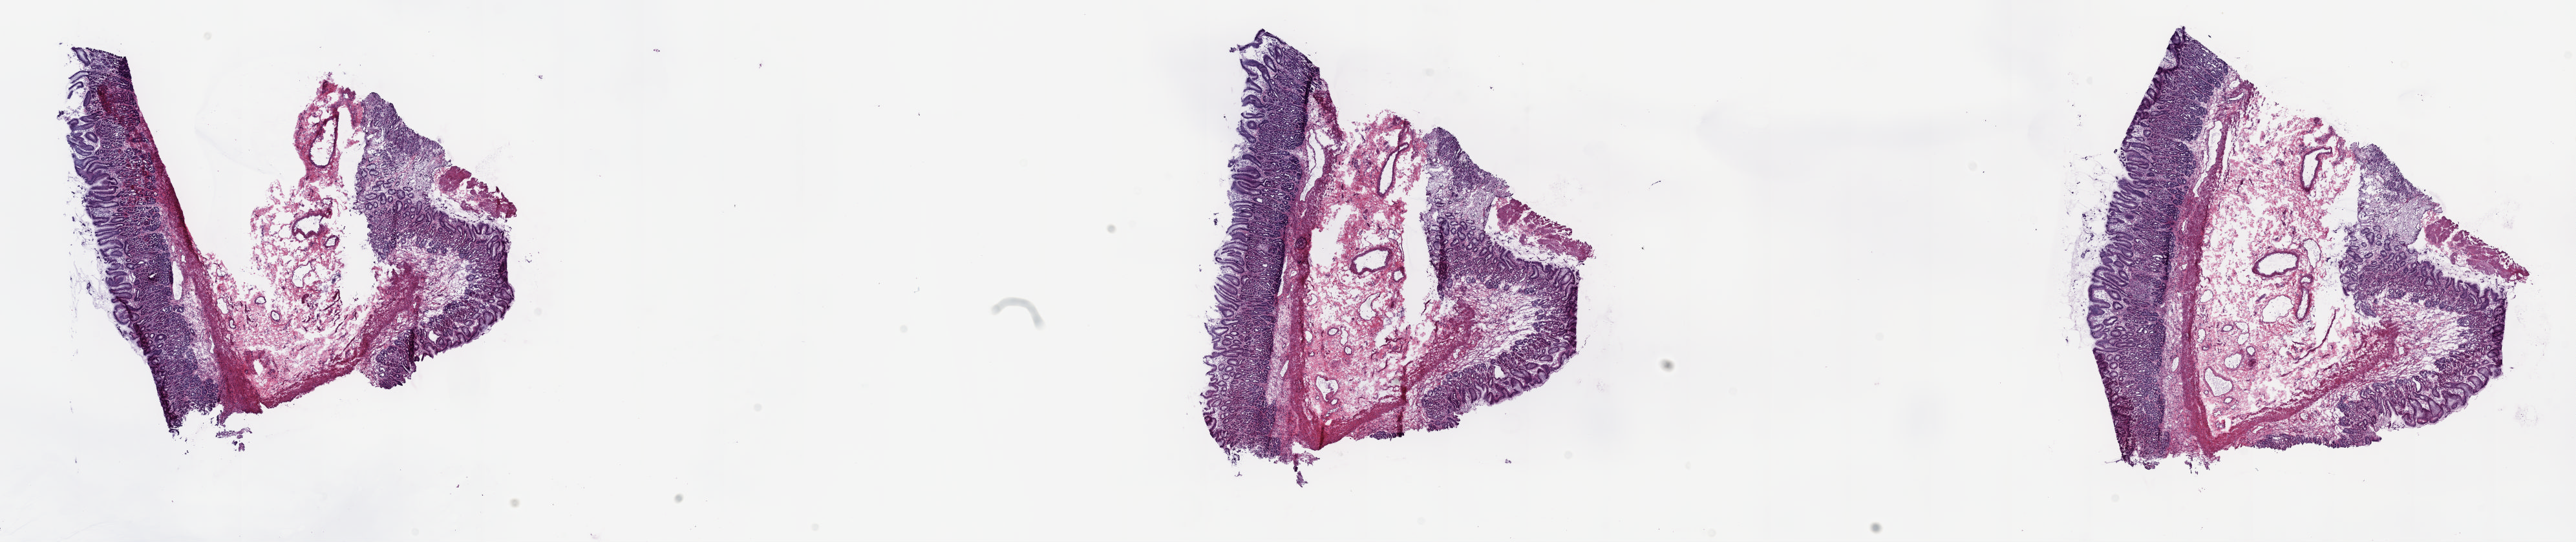
Whole-slide histology image, H&E, low-resolution overview of the scanned area, about 32.1 x 6.8 mm (slide scanned at 20x), frozen section from the top of the tissue portion, solid tissue normal (non-tumour tissue) sample from the esophagus. Patient: male, age at initial diagnosis 69 years. Slide review estimates, as recorded: tumour cells 0%, tumour nuclei 0%, normal cells 100%, stromal cells 0%, necrosis 0%. Infiltration values recorded for this section: lymphocyte infiltration 5%, monocyte infiltration 0%, neutrophil infiltration 0%.
This section: solid tissue normal (non-tumour) sample from the same patient. Patient diagnosis: Adenocarcinoma, NOS.